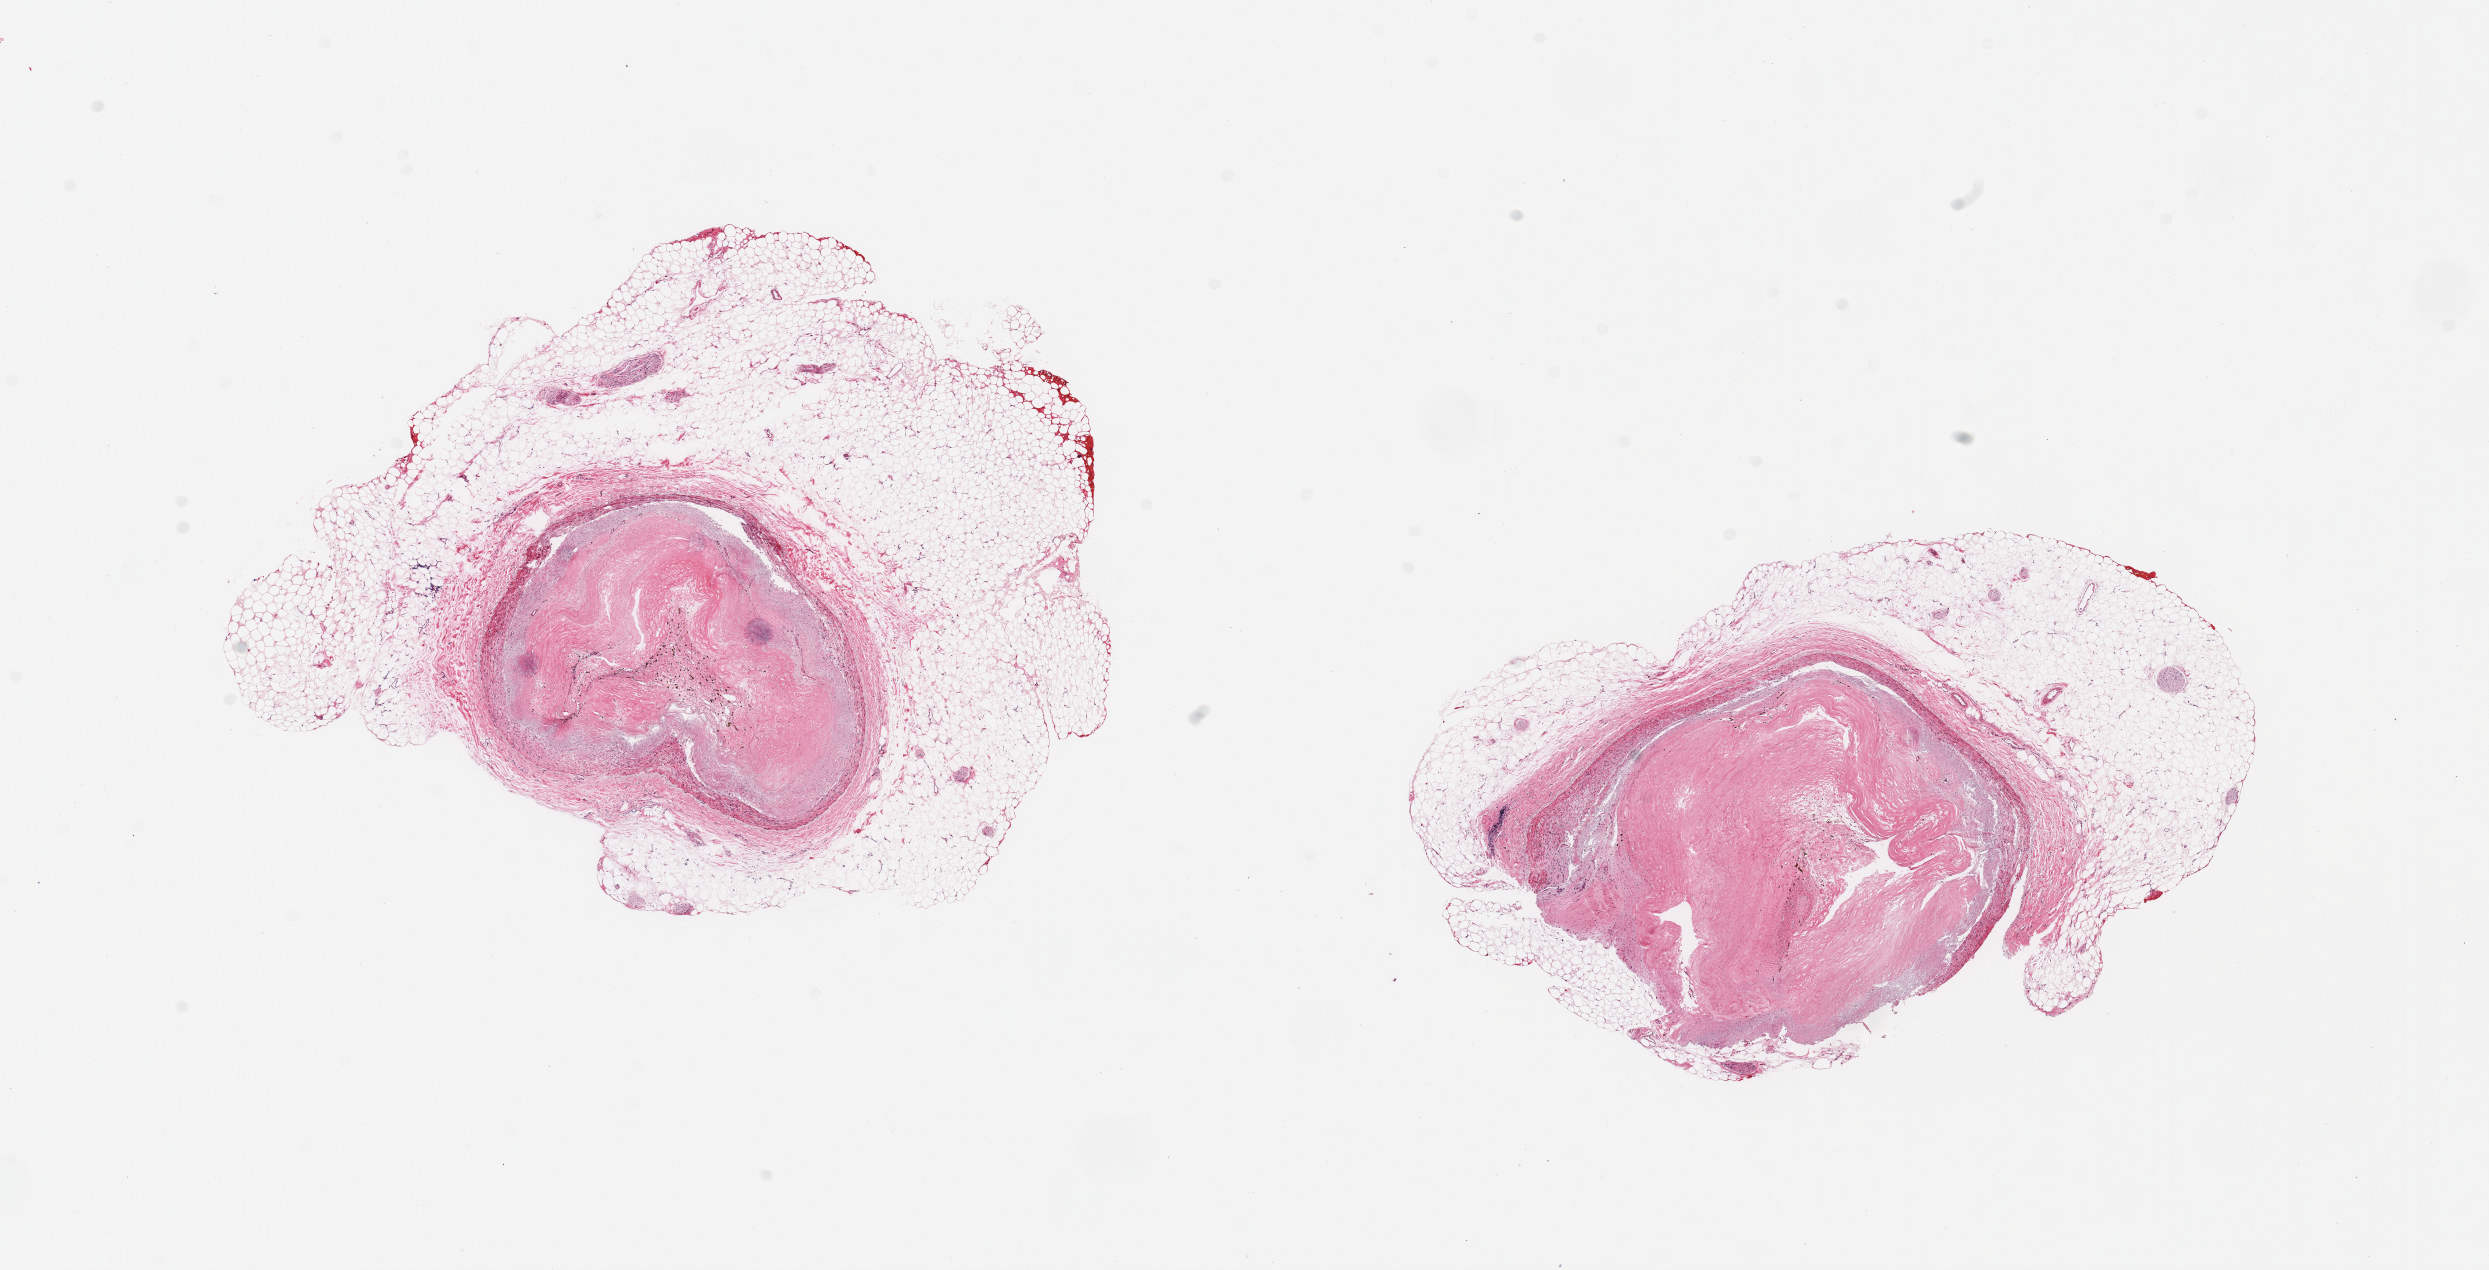
Haematoxylin and eosin whole-slide image, shown as a low-resolution overview of the whole scanned area (about 19.7 x 10.0 mm); PAXgene-fixed, paraffin-embedded tissue; target tissue: coronary artery; tissue donor sample. Male donor.
* pathologist's review note for this sample: 2 pieces; large cuff of adipose tissue (up to 2.2mm), obliterated by plaque